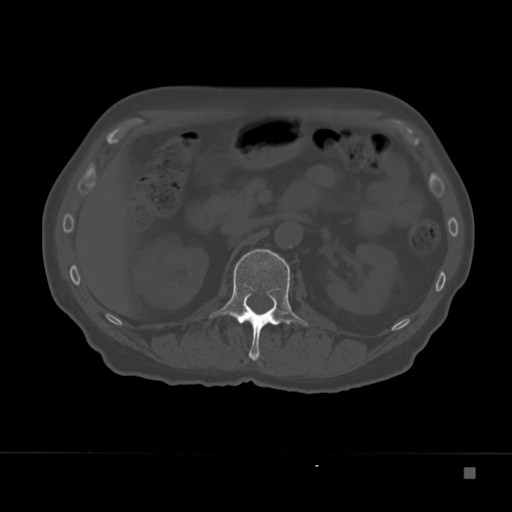
CT including the spine, one axial slice. Slice 111 of 332 in the series (ordered by position). Bone window (W 1800 / L 400 HU). 512 × 512 image matrix. Patient: male, 72 years. Case-level facts recorded for this patient, not image findings: primary cancer: skeletal.
Annotated regions visible in this slice (semi-automatically segmented with operator editing):
- L1 vertebra: box from (x=210, y=249) to (x=308, y=361) px